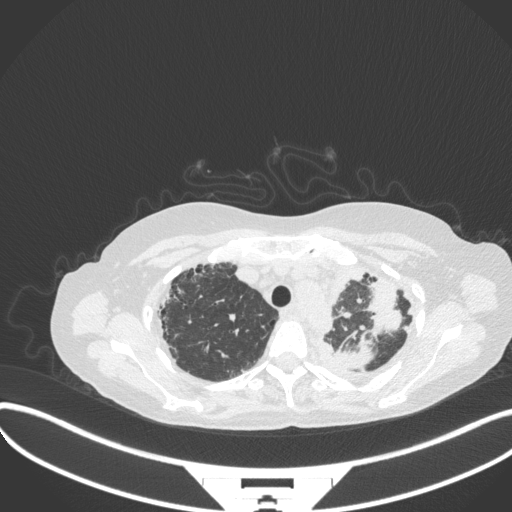
Chest CT, one axial slice; 120 kVp; lung window (W 1500 / L -600 HU); 1 mm slice thickness; 512 × 512 image matrix. Female patient, age 56 years. From the clinical record (not read from this slice): clinical TNM (as recorded): T1 N0 M0.
Outlined on this slice (bounding box drawn by a radiologist):
- lung tumour (recorded histology: adenocarcinoma): bounding box <341,340,372,373> (left, top, right, bottom; pixels)
- lung tumour (recorded histology: adenocarcinoma): <363,278,406,341>